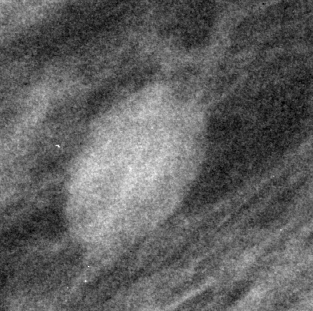
Crop from a digitized film mammogram around one marked abnormality, right breast, MLO view.
- Finding: mass, shape oval, margins circumscribed; BI-RADS assessment category 3; subtlety rating 5 on a 1 (subtle) to 5 (obvious) scale; pathology result (as recorded, not read from the image): benign.